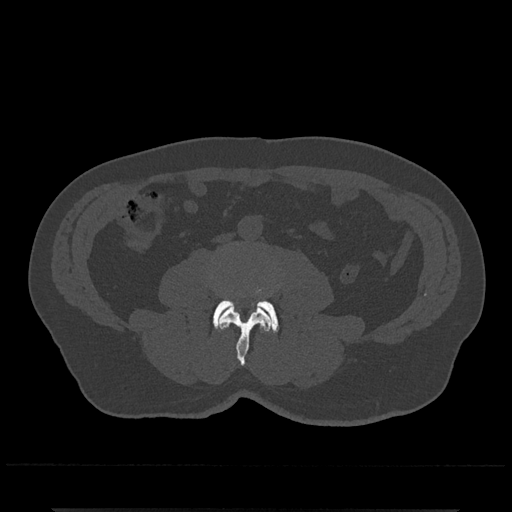
CT including the spine, one axial slice; slice 192 of 797 in the series (ordered by position); reconstruction kernel Br40s/3; bone window (W 1800 / L 400 HU); 0.5 mm slice thickness; 512 × 512 image matrix, field of view 393 × 393 mm. Patient: male, 67 years. Case-level facts recorded for this patient, not image findings: primary cancer: prostate.
Outlined on this slice (semi-automatically segmented with operator editing):
- L3 vertebra: bounding box [x1, y1, x2, y2] px = [218, 306, 272, 365]
- L4 vertebra: [212, 289, 279, 332]